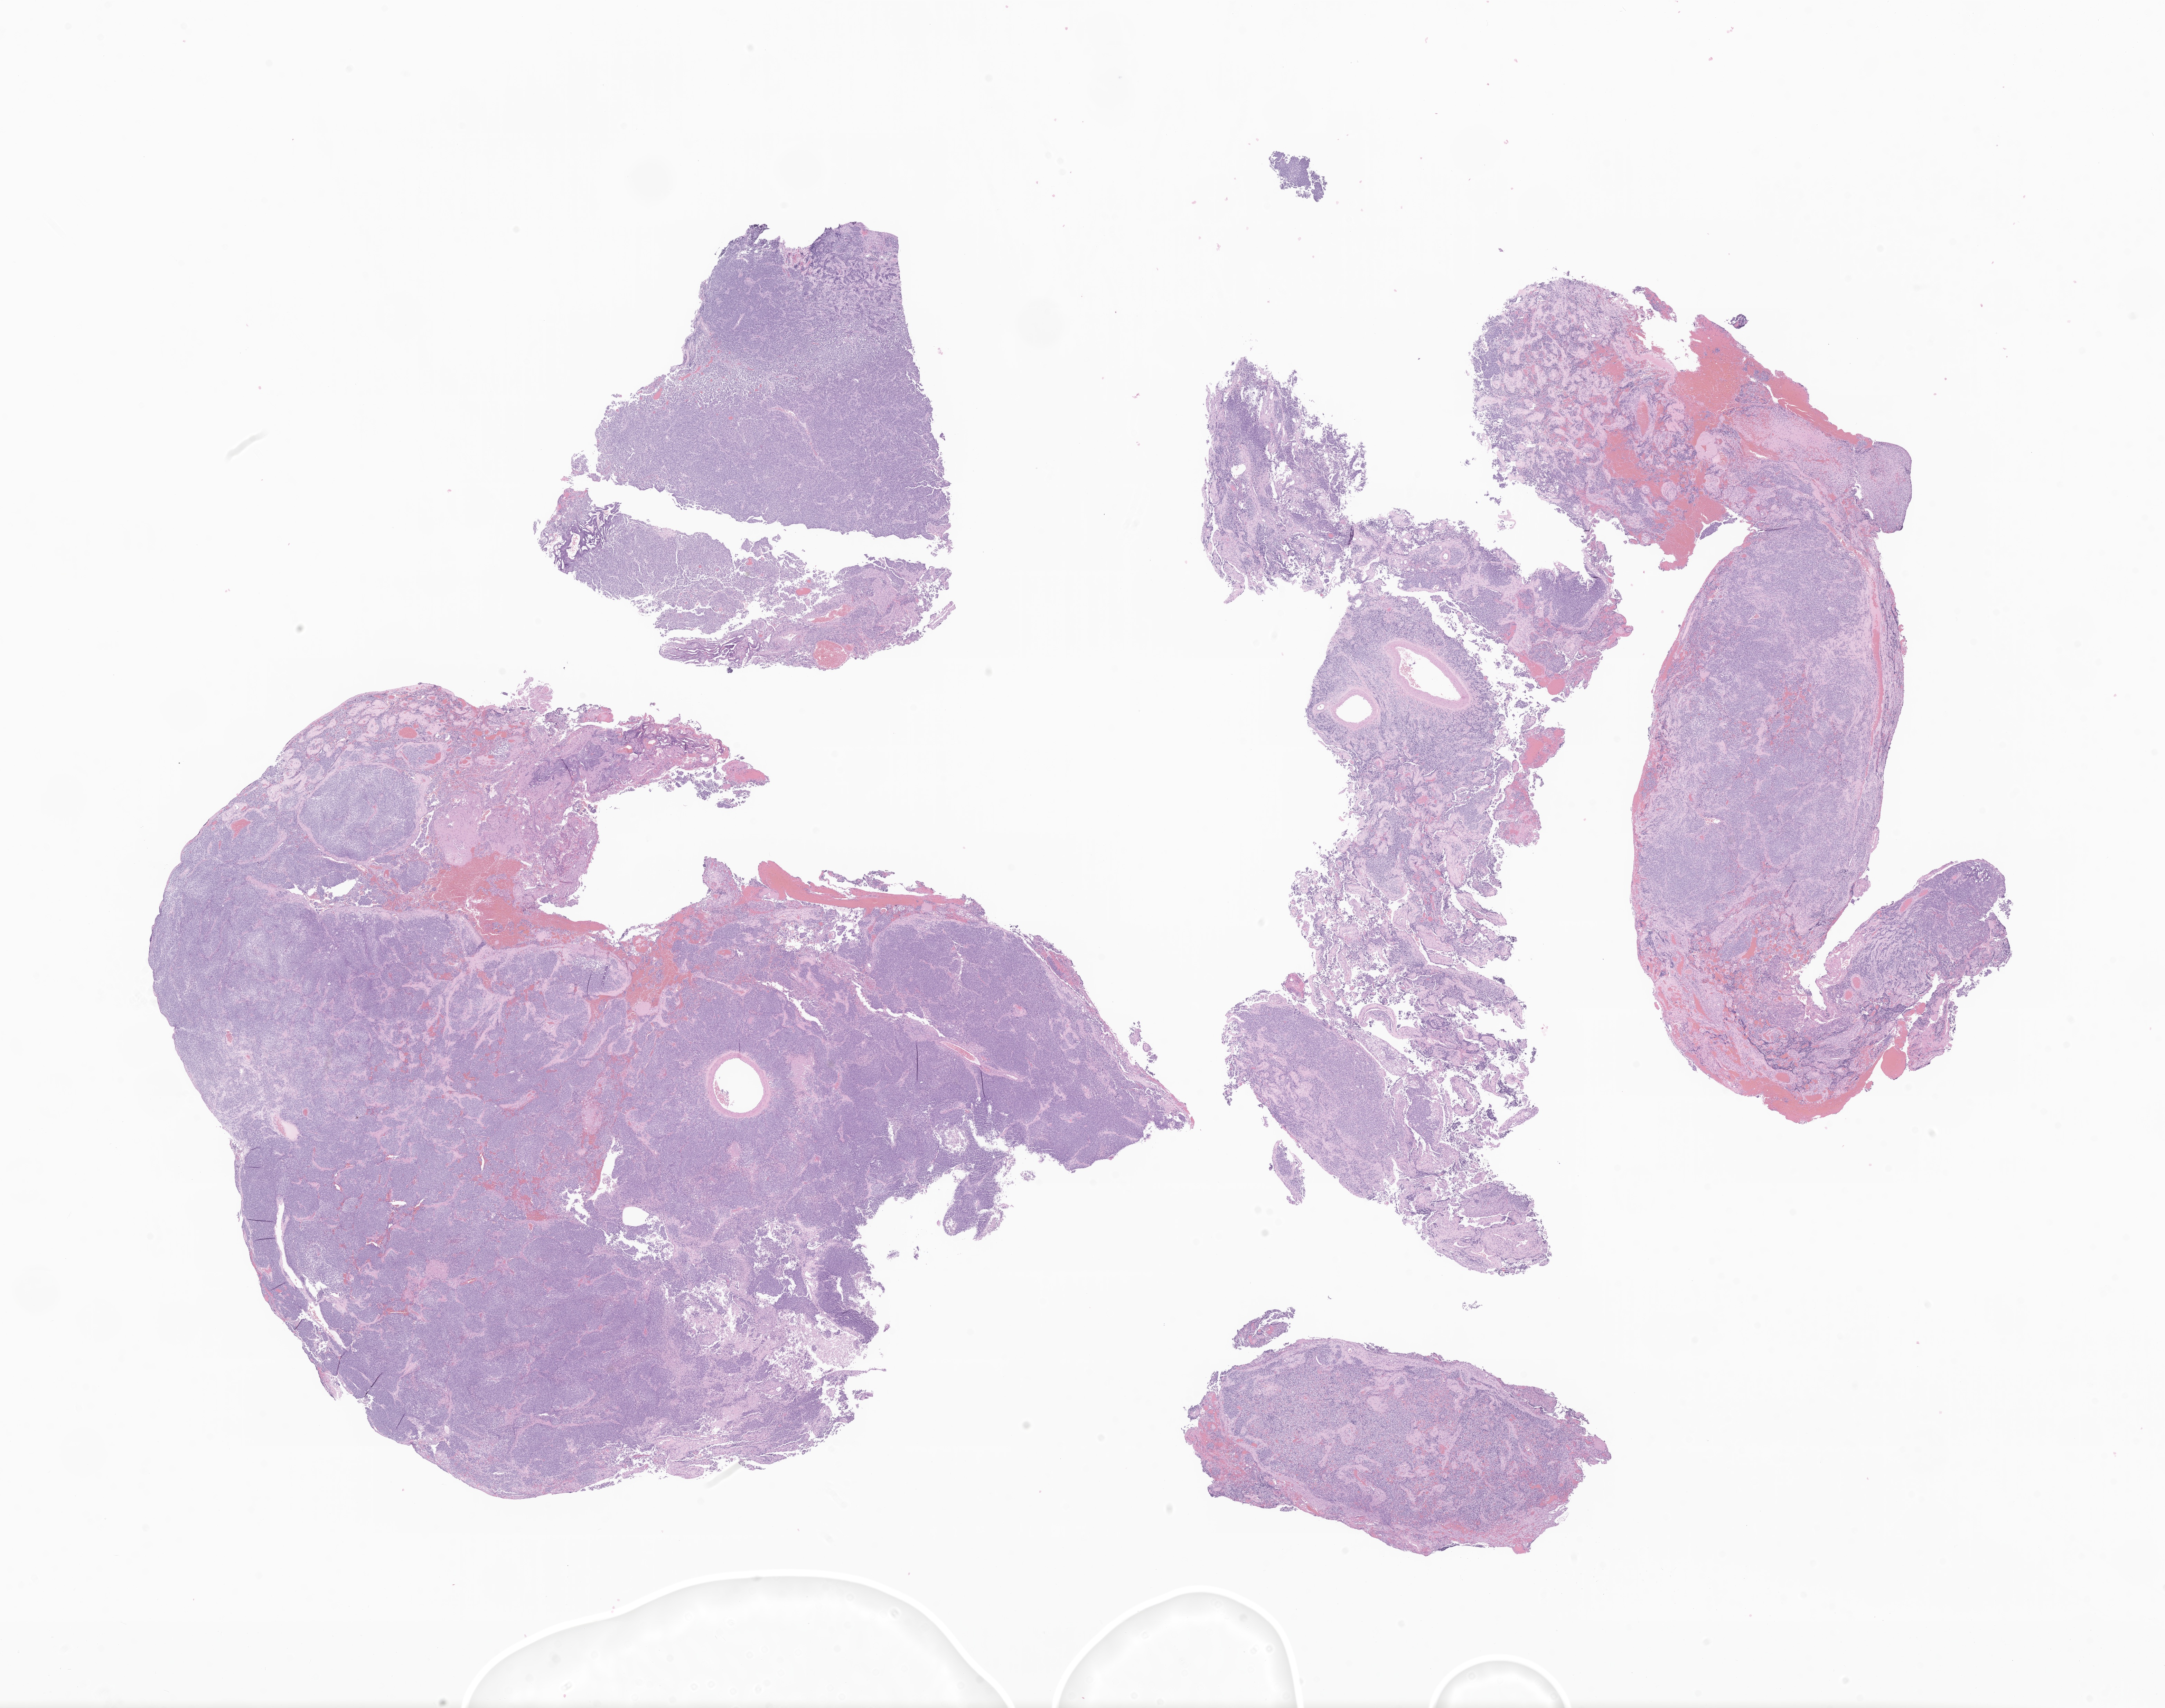
Digitized haematoxylin and eosin-stained section of tumor tissue from the brain, low-resolution overview of the scanned area, about 26.4 x 20.8 mm; FFPE section. Patient: male, age 155 months (12 years 11 months).
Recorded diagnosis: Medulloblastoma, NOS.